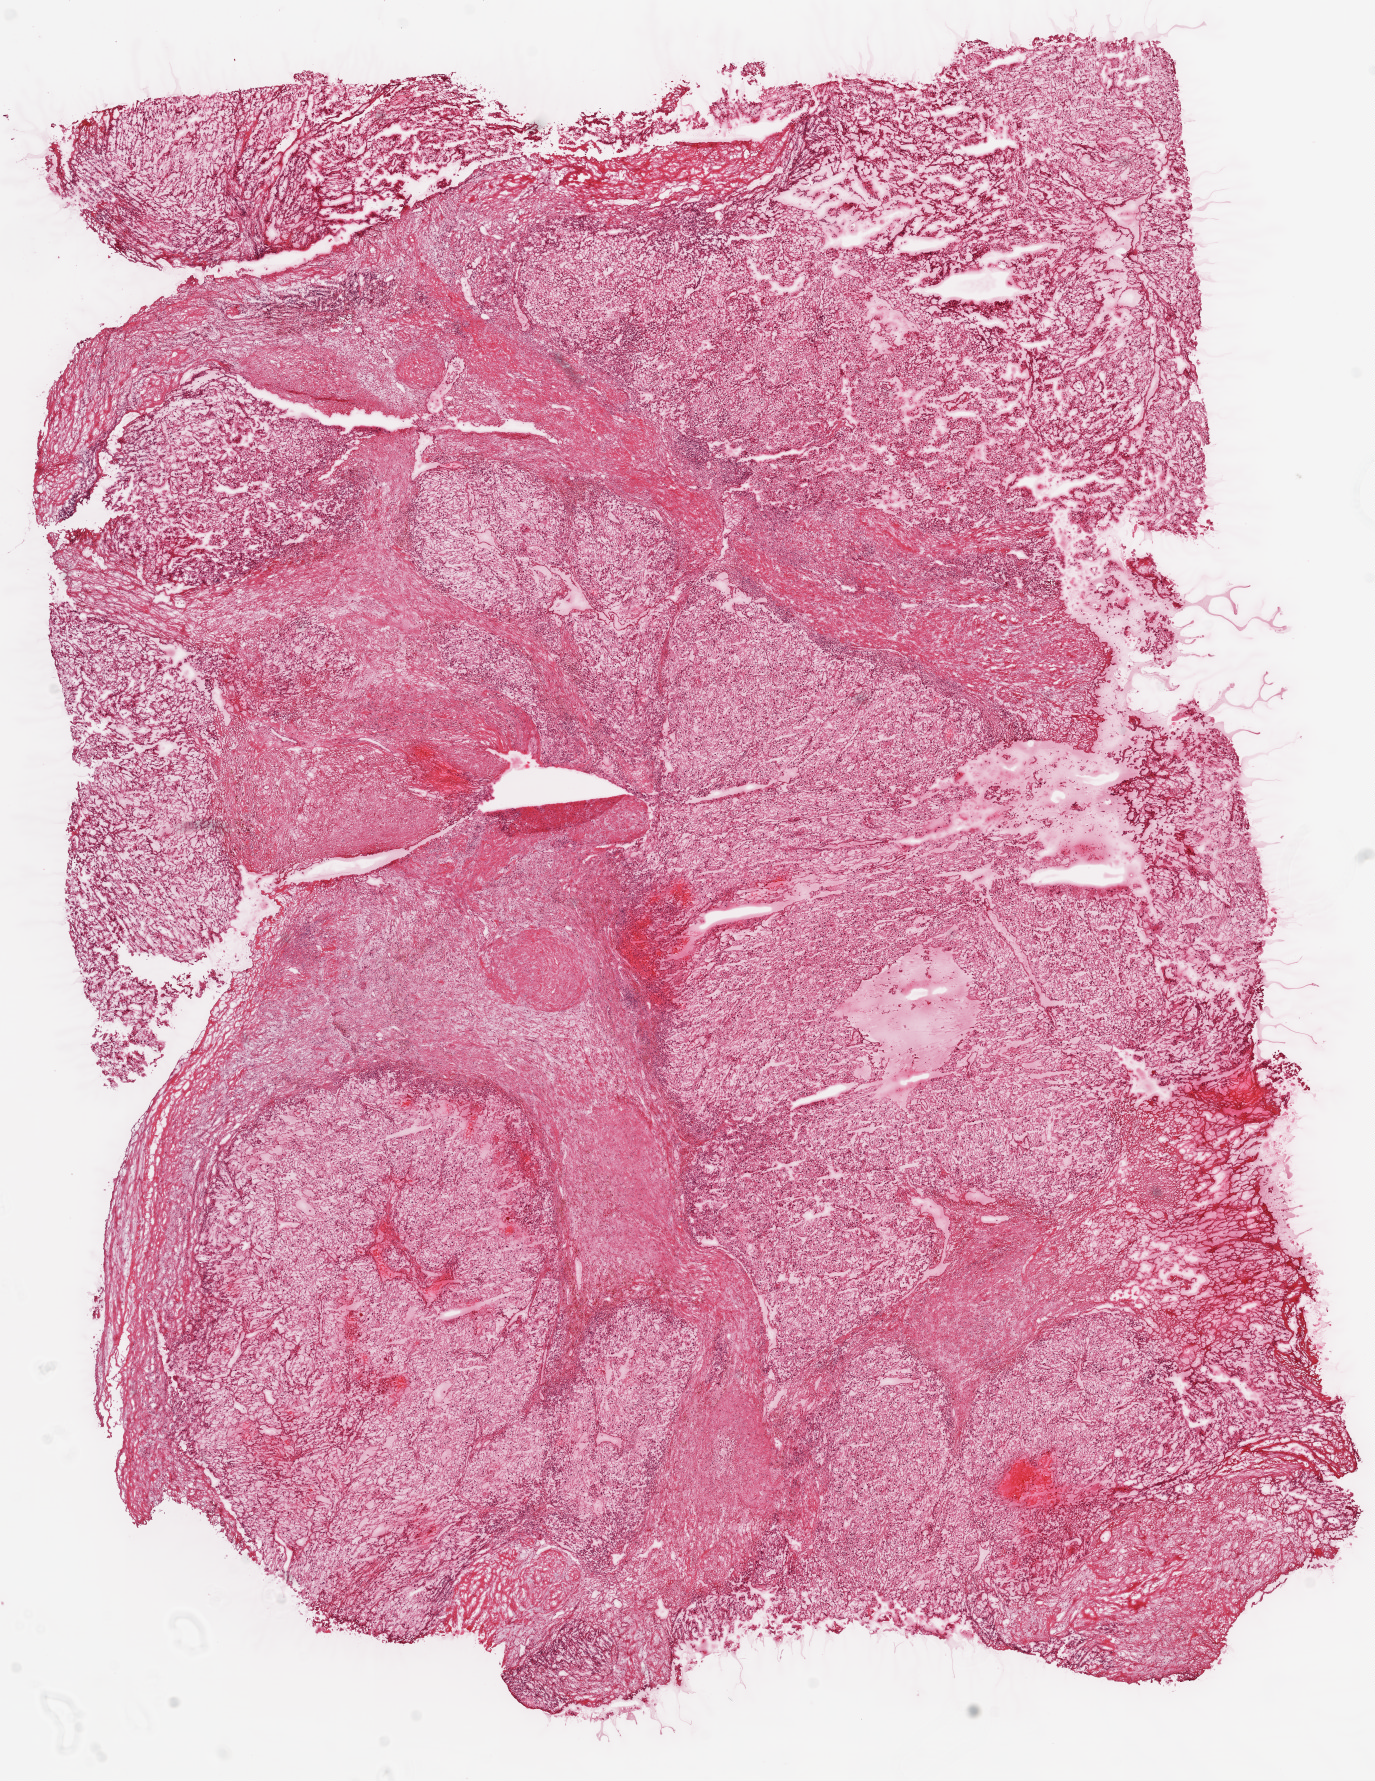
Hematoxylin and eosin (H&E) stained whole-slide image — a low-resolution overview of the entire scanned area, about 11.0 x 14.3 mm; frozen section from the top of the tissue portion; primary tumour sample from the kidney. Patient: male, age at initial diagnosis 59 years. Histologic grade: G2 (moderately differentiated). Pathologist review of this section (percent, as recorded): tumour cells 85%, tumour nuclei 90%, normal cells 0%, stromal cells 15%, necrosis 0%.
- diagnosis: Clear cell adenocarcinoma, NOS
- AJCC pathologic stage: III